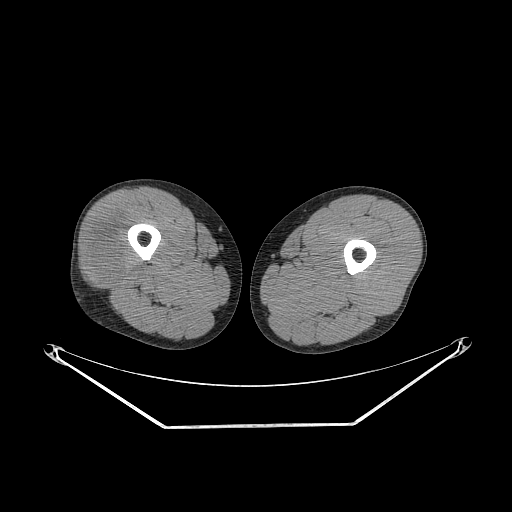
CT of an extremity soft-tissue mass (from a PET/CT study), one axial slice; position 232 of 267 along the scan axis; reconstruction kernel STANDARD; 140 kVp; soft-tissue window (W 400 / L 40 HU); 3.75 mm slice thickness; 512 × 512 image matrix, field of view 500 × 500 mm. Male patient. Case-level facts recorded for this patient, not image findings: histological type: poorly differentiated synovial sarcoma; grade: high; site of the primary tumour: right buttock.
Outlined on this slice (expert contour drawn on MRI and transferred to this co-registered scan by the dataset authors):
- gross tumour volume including surrounding oedema: bounding box (x1, y1, x2, y2) in pixels: (89, 226, 140, 284)
- gross tumour volume (mass): (91, 230, 129, 282)